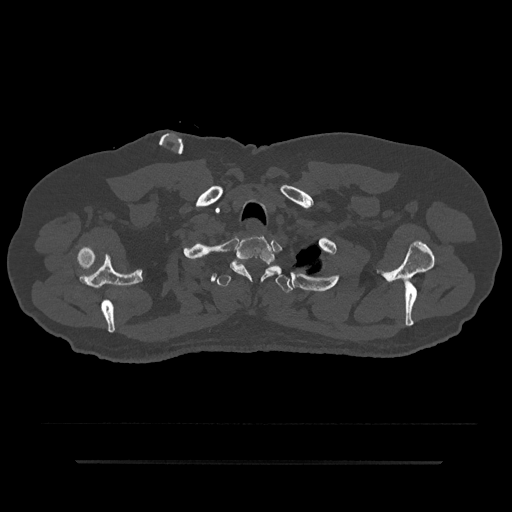
CT including the spine, one axial slice; position 724 of 797 along the scan axis; reconstruction kernel Br40s/3; 120 kVp; bone window (W 1800 / L 400 HU); 512 × 512 image matrix. Patient: male, 59 years. From the clinical record (not read from this slice): primary cancer: bile ducts; vertebrae with lytic lesions (as recorded): T10.
Structures marked on this image (semi-automatically segmented with operator editing):
- T1 vertebra: box from (x=230, y=236) to (x=276, y=281) px
- T2 vertebra: (x=216, y=265)–(x=292, y=293)